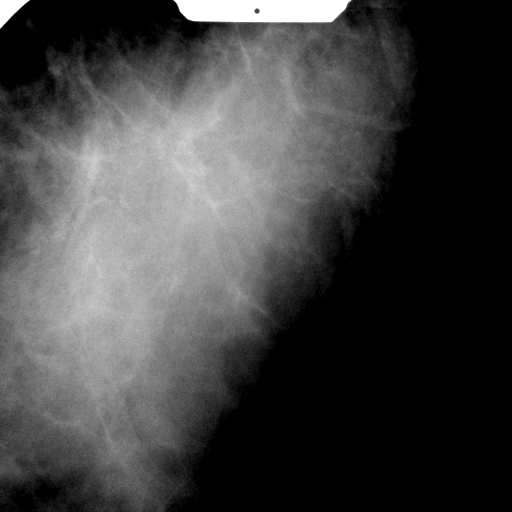
Spot-compression mammographic view.
Pathology recorded for this patient (not read from this image): pathology diagnosis: benign fibroadenoma (right breast); pathology report notes: RIGHT BREAST CALCIFICATION WITH NEEDLE LOCATION: FIBROADENOMA (1.9CM). REMAINING BREAST TISSUE WITH ADENOSIS, FOCAL FIBROADENOMATOUS CHANGES, APOCRINE METAPLASIA, FIBROCYSTIC CHANGES, SMALL INTRADUCTAL PAPILLOMAS, AND USUAL TYPE DUCTAL HYPERPLASIA. MICROCALCIFICATIONS ASSOCIATED WITH BENIGN BREAST TISSUE ARE IDENTIFIED. NO IN-SITU OR INVASIVE CARCINOMA.